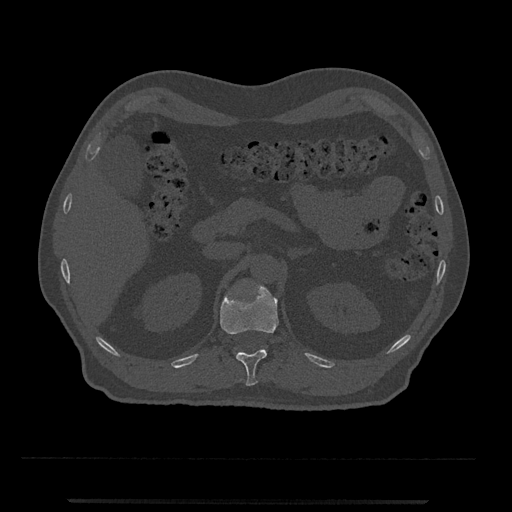
CT including the spine, one axial slice; position 384 of 797 along the scan axis; reconstruction kernel Br40s/3; 120 kVp; bone window (W 1800 / L 400 HU); 0.5 mm slice thickness; 512 × 512 image matrix, field of view 419 × 419 mm. Patient: male, 63 years. Case-level facts recorded for this patient, not image findings: primary cancer: prostate.
Outlined on this slice (semi-automatic segmentation, software-assisted and operator-edited):
- T12 vertebra: bounding box <220,284,279,386> (left, top, right, bottom; pixels)